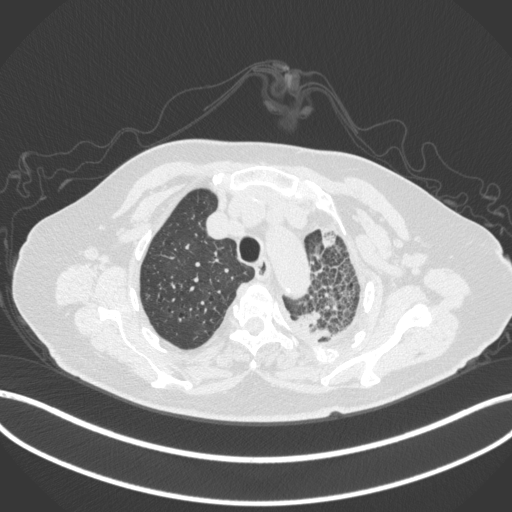
Chest CT, one axial slice; slice 319 of 399 in the series (ordered by position); 120 kVp; lung window (W 1500 / L -600 HU); 1 mm slice thickness; 512 × 512 image matrix, field of view 400 × 400 mm. Patient: female, 75 years. Case-level facts recorded for this patient, not image findings: clinical TNM (as recorded): T3 N3 M1.
Structures marked on this image (bounding box drawn by a radiologist):
- lung tumour (recorded histology: adenocarcinoma): box from (x=293, y=305) to (x=337, y=352) px